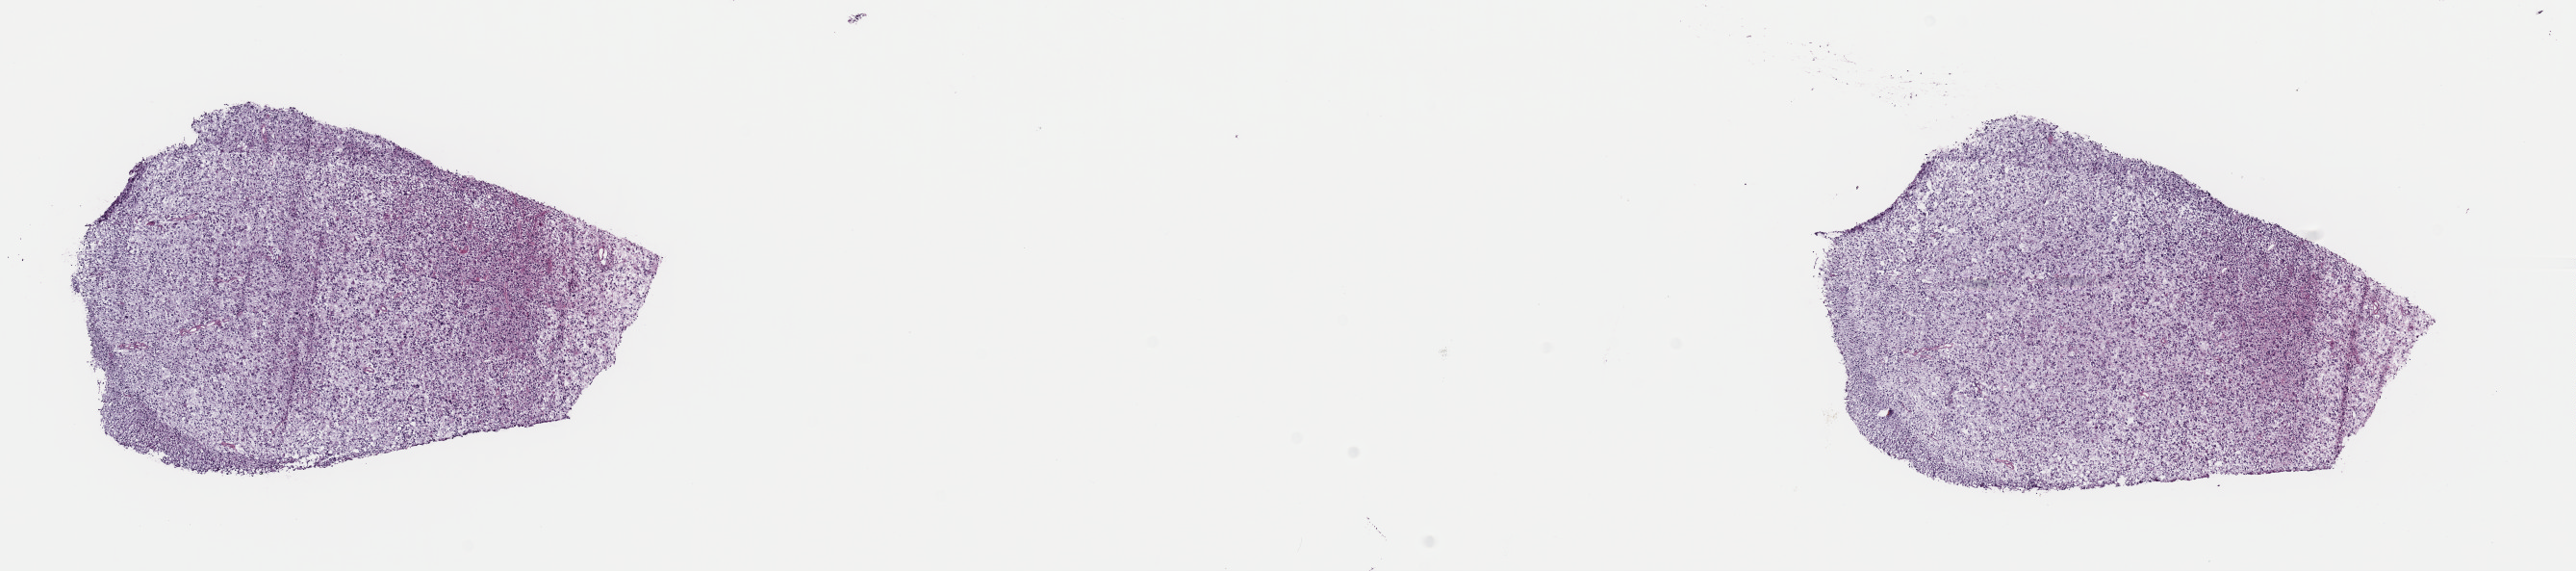
H&E whole-slide image, whole scanned area (about 21.1 x 4.7 mm) shown as a low-resolution overview, frozen section from the top of the tissue portion, brain, primary tumour sample. Female patient; age at initial diagnosis 56 years. Histologic grade: G3 (poorly differentiated). Composition of this section per pathologist review: tumour cells 75%, tumour nuclei 90%, normal cells 5%, stromal cells 20%, necrosis 0%. Infiltration values recorded for this section: lymphocyte infiltration 0%, monocyte infiltration 0%, neutrophil infiltration 0%.
- pathologic diagnosis: Astrocytoma, anaplastic (cerebrum)
- laterality: right